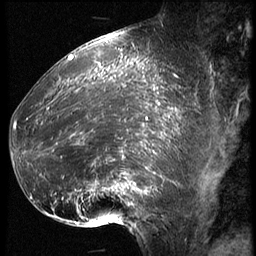
Breast MRI (dynamic contrast-enhanced), one sagittal slice; slice 24 of 62 in the series (ordered by position); 3 images stored at this slice position (order not interpretable as contrast timing); 1.5 T; TE 4.2 ms, TR 9 ms; 256 × 256 image matrix. Patient: female, 39 years. Case-level facts recorded for this patient, not image findings: setting: breast cancer imaged before/during neoadjuvant chemotherapy; receptor status: HER2-positive.
Annotated regions visible in this slice (semi-automatically segmented with operator editing):
- analysis volume of interest (the breast-tissue region the enhancement analysis was run in; not a lesion): bounding box [x1, y1, x2, y2] px = [16, 64, 171, 228]
- tumour enhancement mask (voxels above the 140 % enhancement threshold inside the analysis volume of interest): [16, 64, 171, 224]